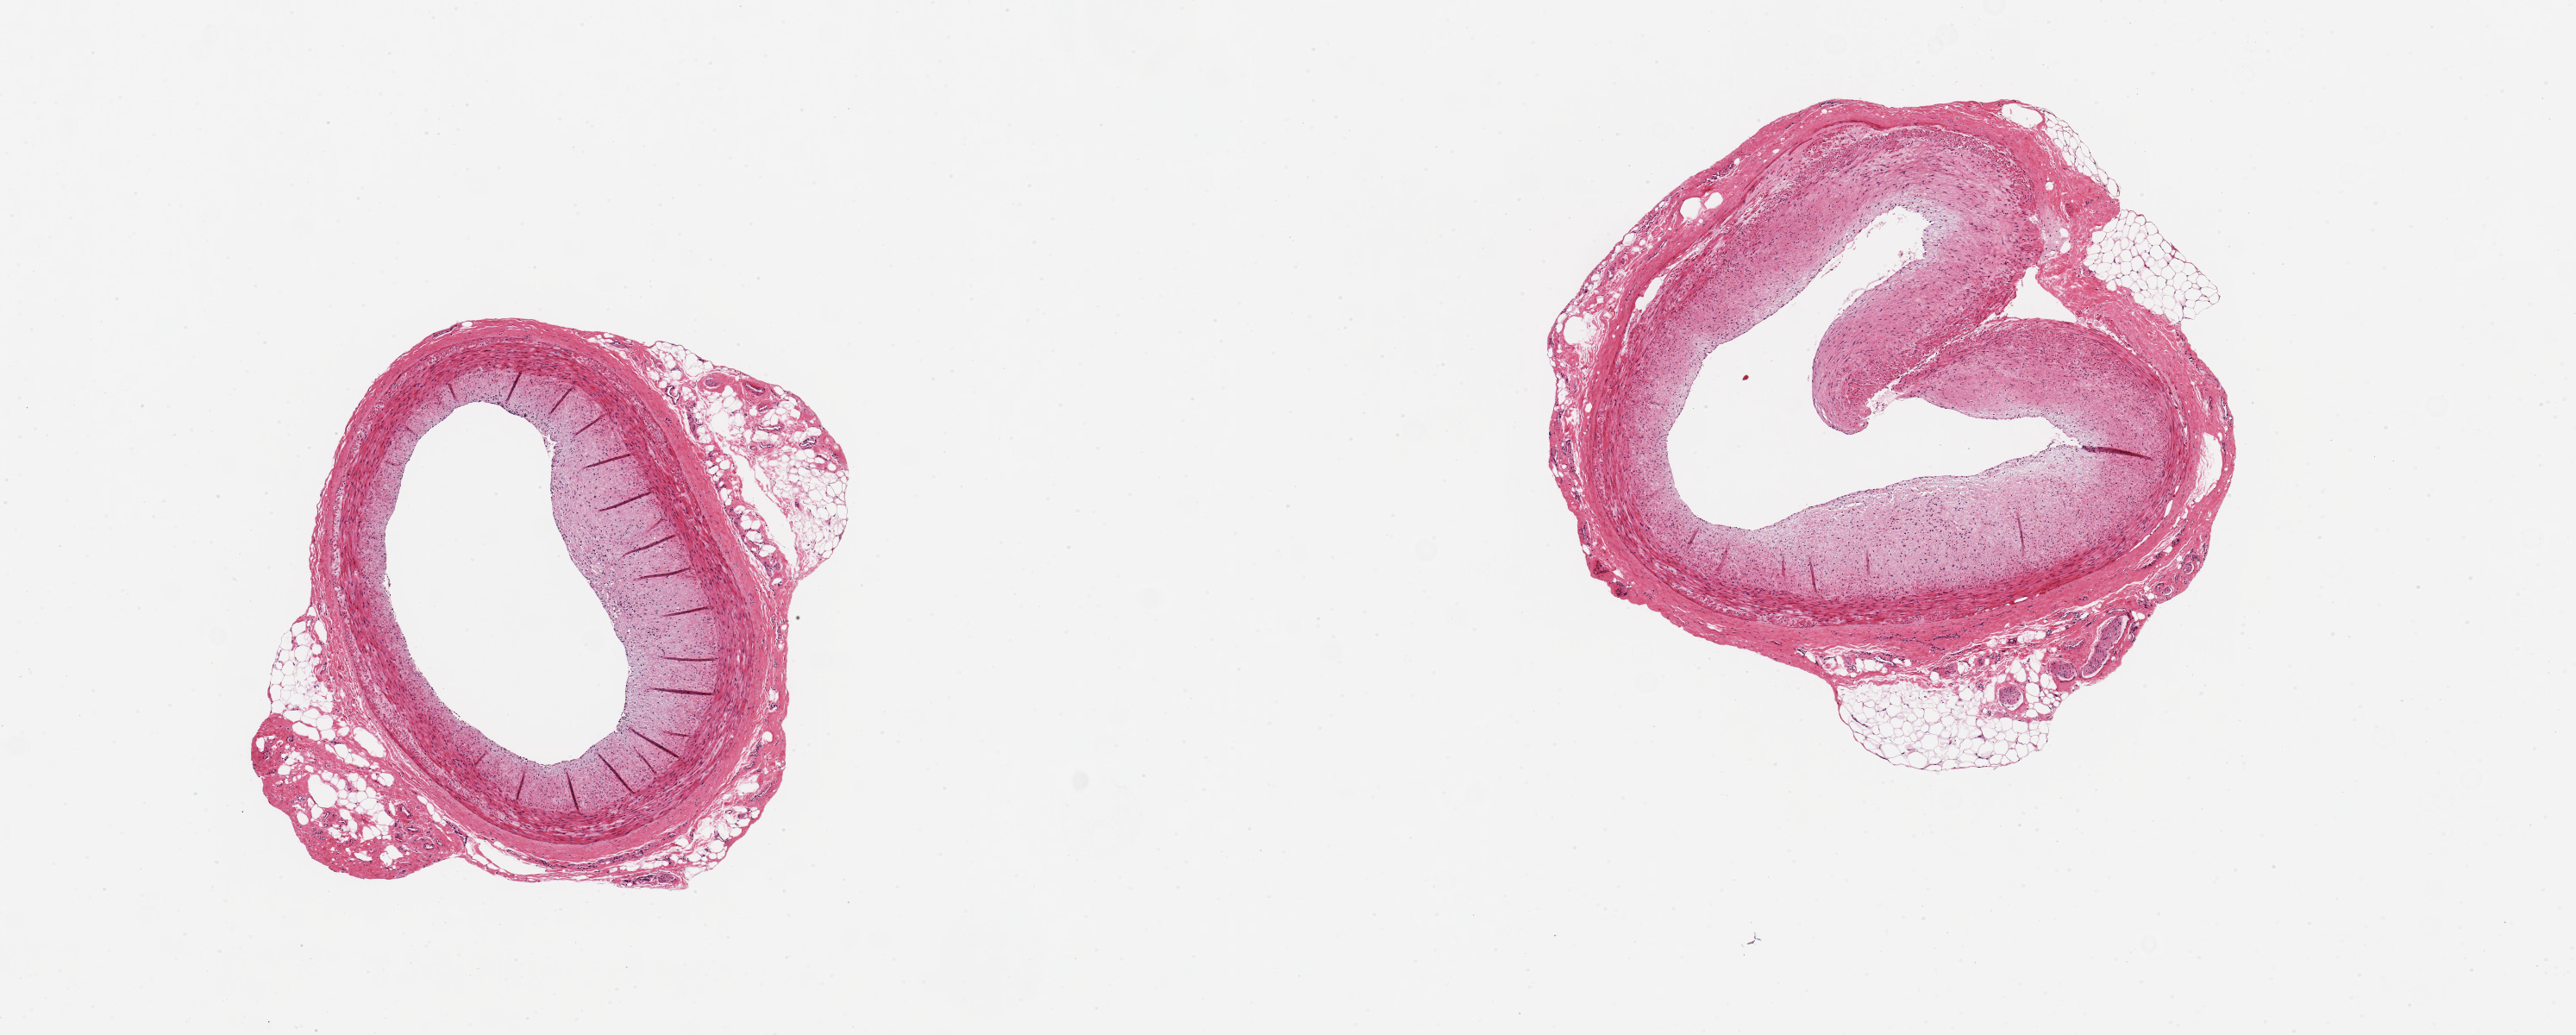
Digitized hematoxylin and eosin (H&E)-stained section, a low-resolution overview of the entire scanned area, about 11.8 x 4.7 mm (slide scanned at 20x), PAXgene-fixed, paraffin-embedded tissue, section of coronary artery (target tissue), tissue donor sample. Donor sex: male.
Pathologist's review note for this sample: 2 pieces, ~2.5 mm arteries with focal eccentric plaques; ~20% peripheral adipose tissue.